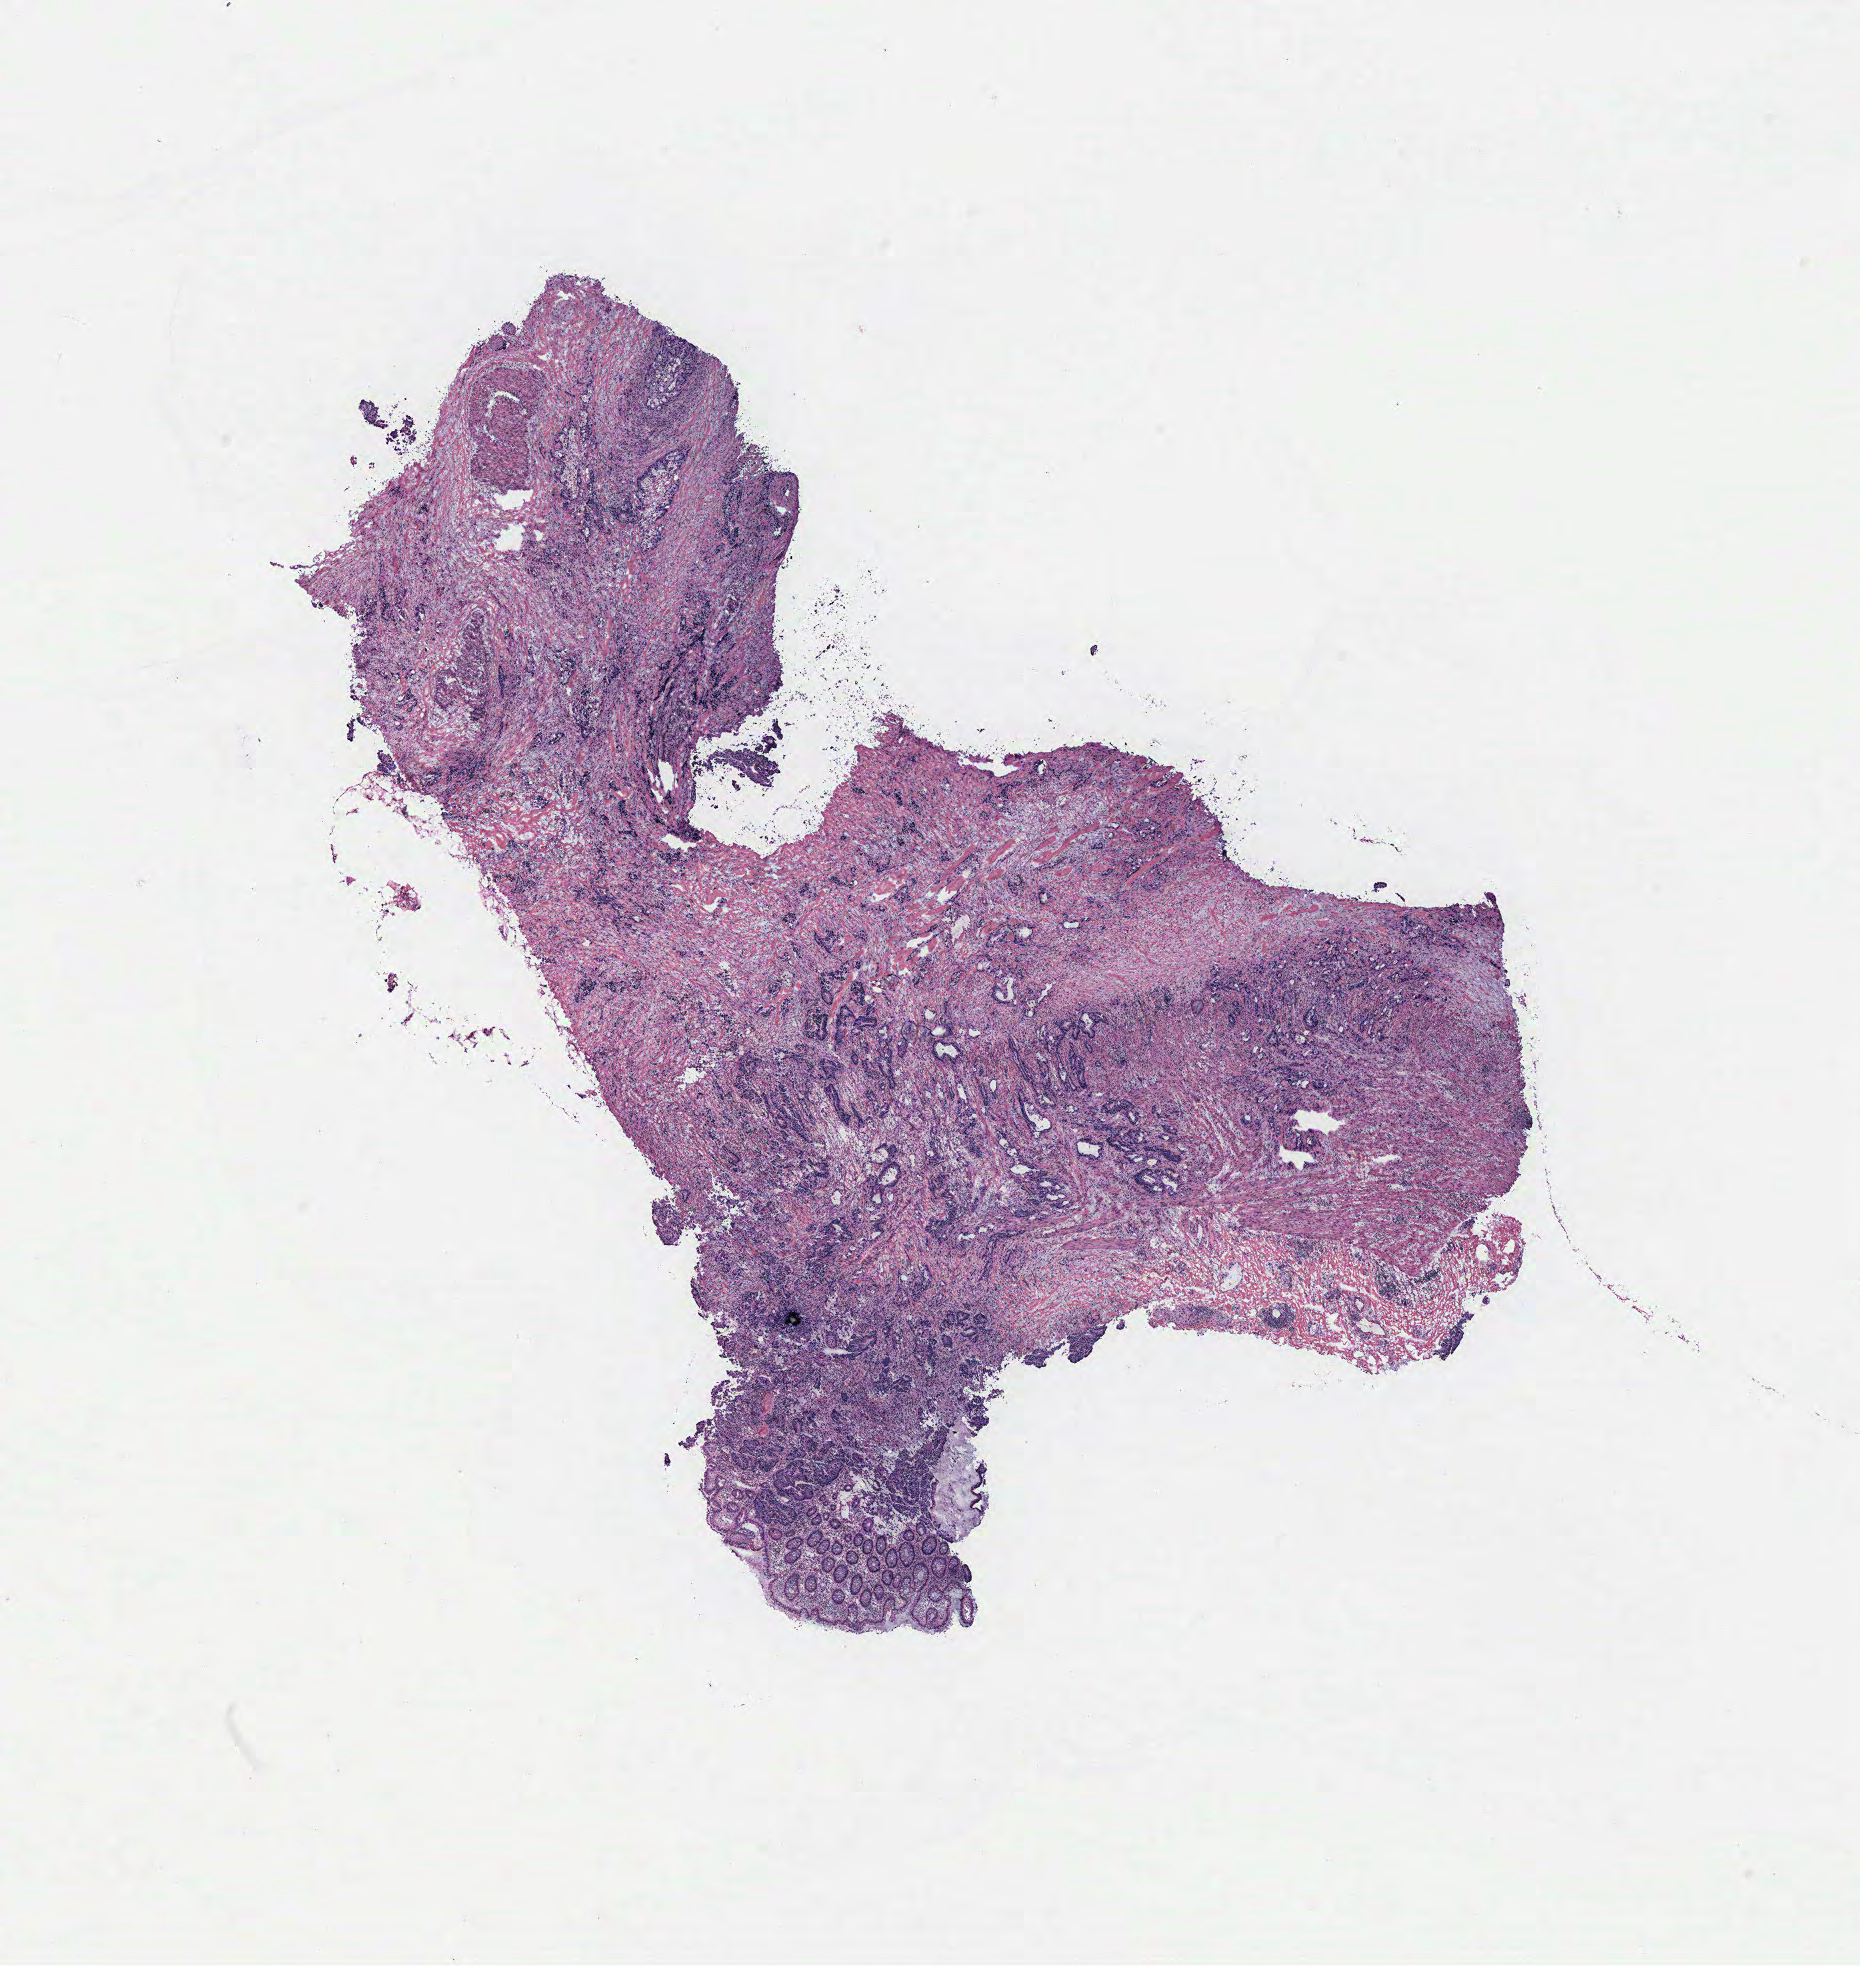
Hematoxylin and eosin (H&E) stained whole-slide image — a low-resolution overview of the entire scanned area, about 14.9 x 15.7 mm (from a 40x scan), colon, normal (non-tumour) tissue. 53-year-old female patient.
* this section: normal (non-tumour) tissue from the same patient
* patient diagnosis: Adenocarcinoma, NOS